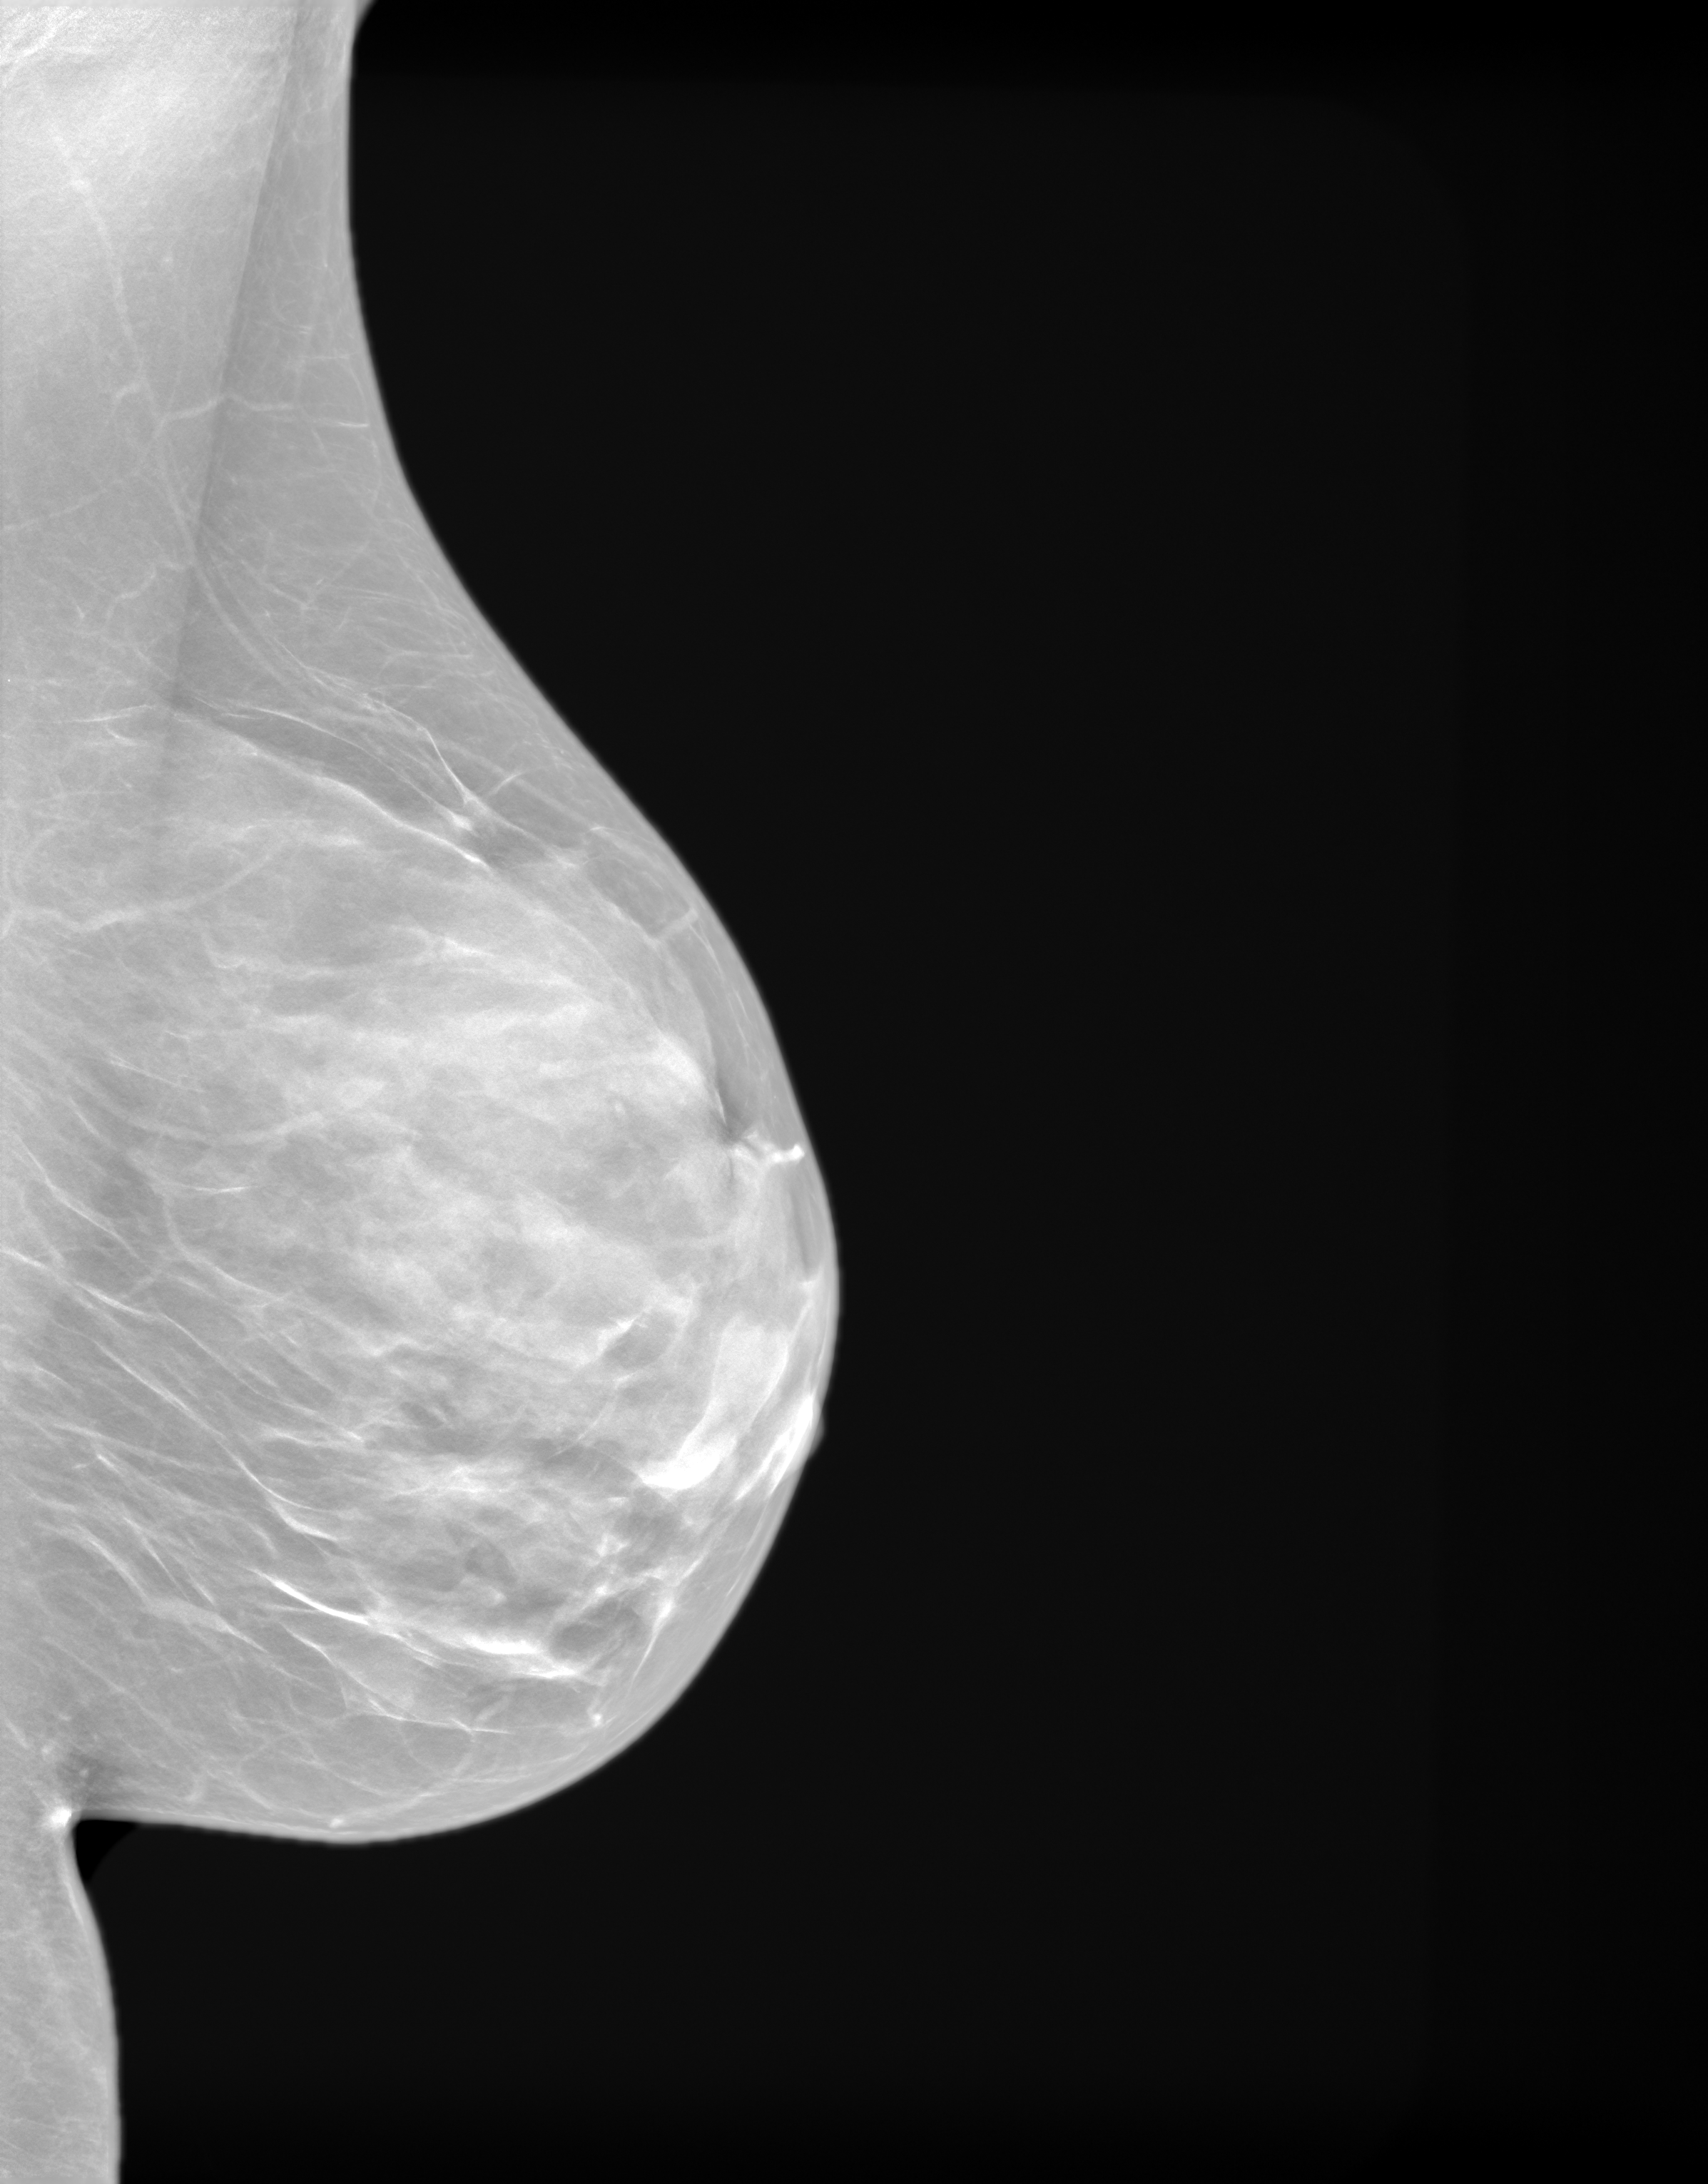
Screening examination. Patient: female, 61 years.
Image type: synthesized 2-D view from tomosynthesis. Breast: left. Projection: mediolateral oblique (MLO) view.